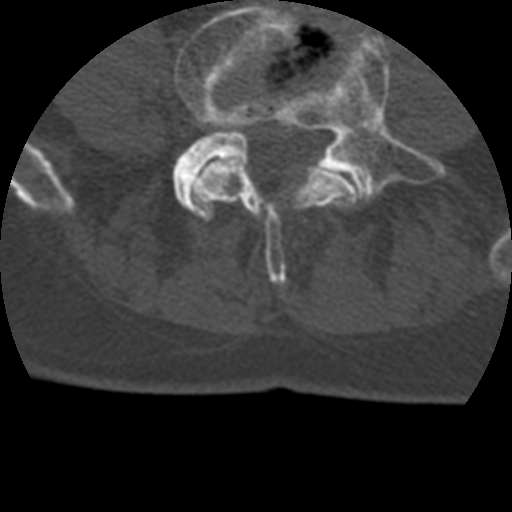
CT including the spine, one axial slice. Slice 54 of 399 in the series (ordered by position). Bone window (W 1800 / L 400 HU). 1.25 mm slice thickness. 512 × 512 image matrix, field of view 160 × 160 mm. Patient age 69 years. Case-level facts recorded for this patient, not image findings: primary cancer: prostate.
Outlined on this slice (semi-automatically segmented with operator editing):
- L4 vertebra: box from (x=175, y=0) to (x=359, y=288) px
- L5 vertebra: (x=172, y=30)–(x=432, y=210)